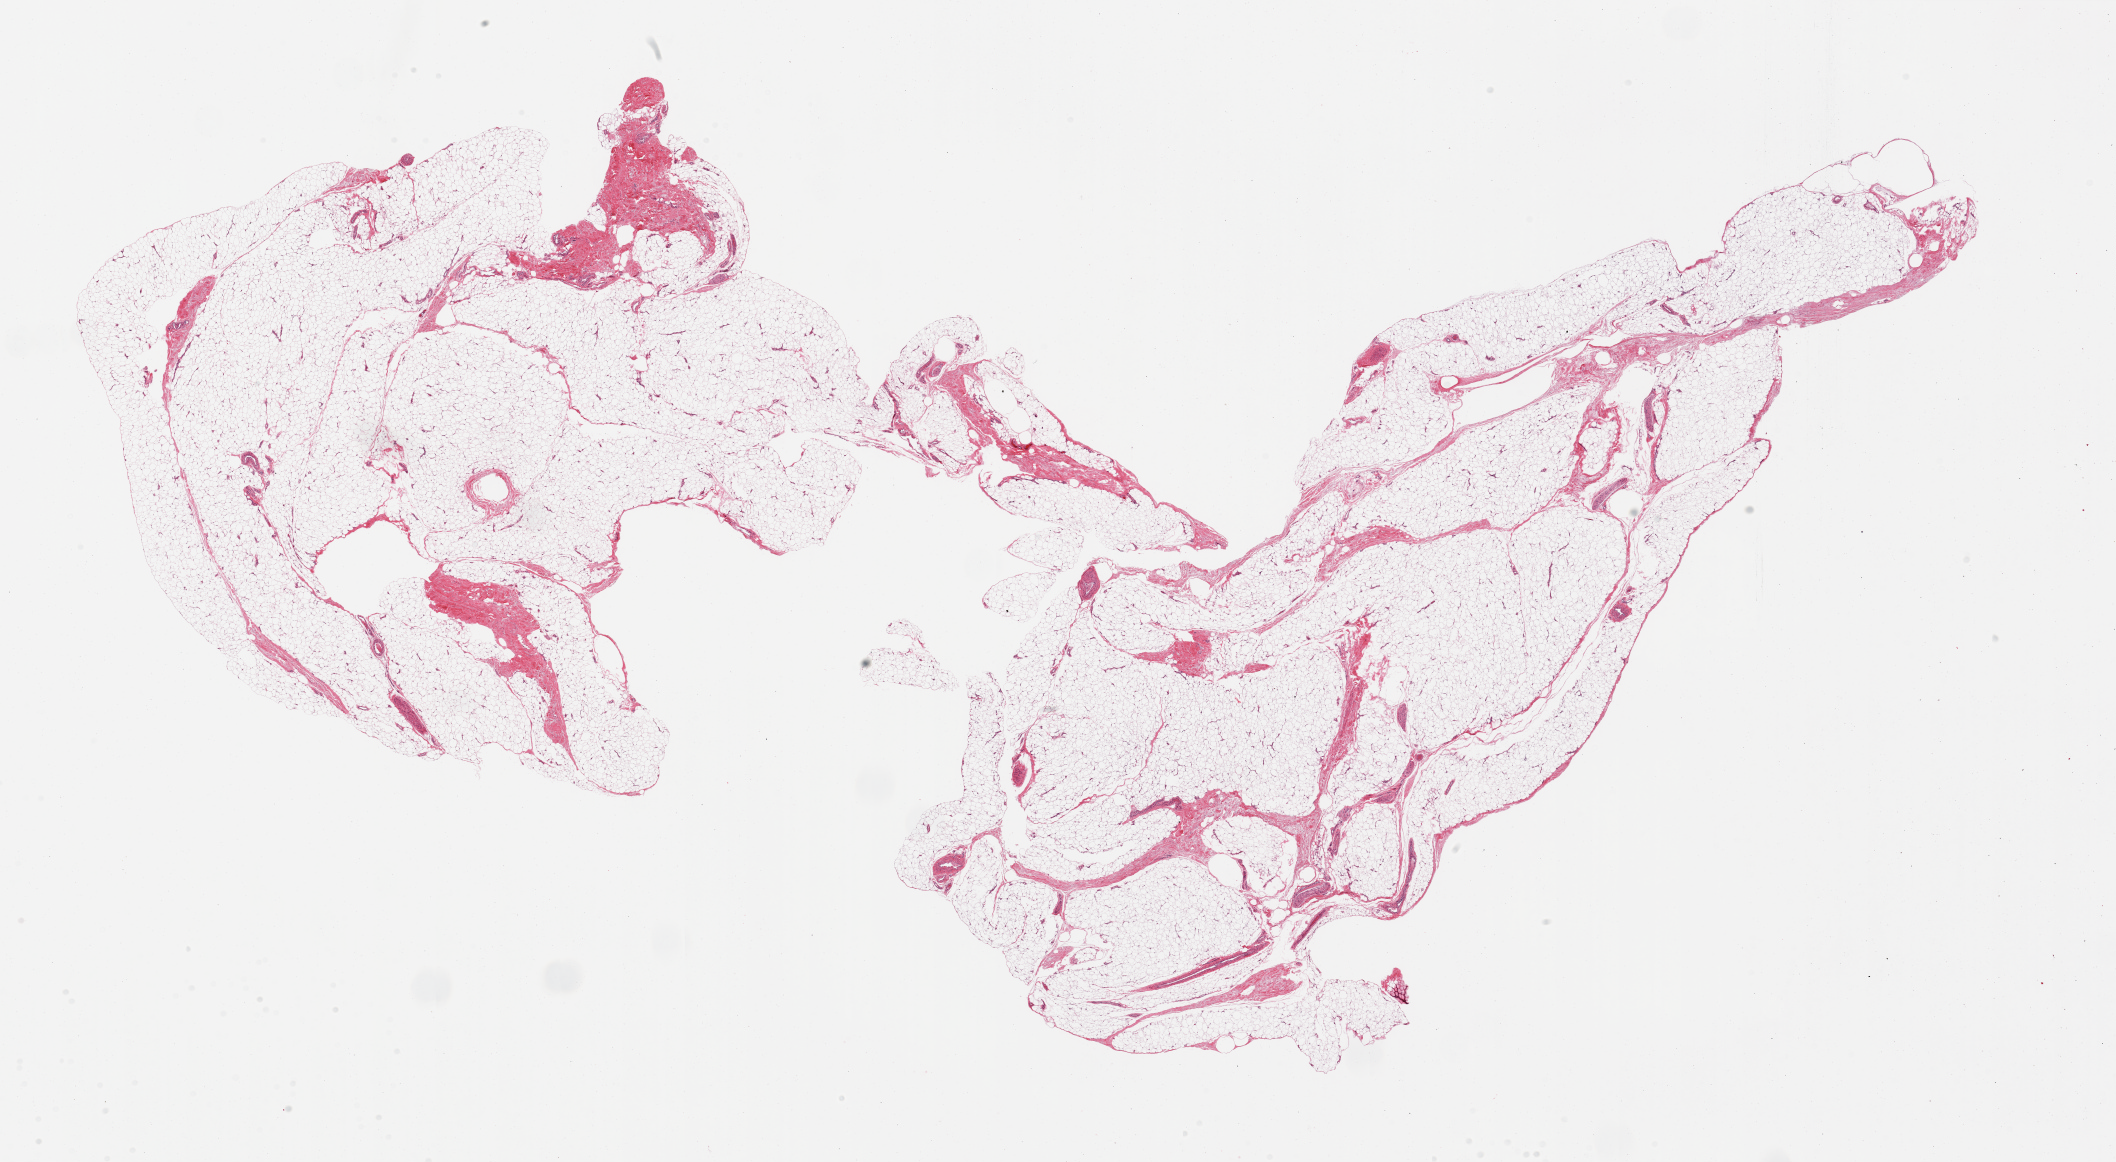
H&E whole-slide image — a low-resolution overview of the entire scanned area, about 33.5 x 18.4 mm, PAXgene-fixed, paraffin-embedded tissue, target tissue: adipose tissue, donor tissue sample. Donor: male.
- review note (as recorded): 2 pieces, ~10% interstitial fascial/fibrous tissue